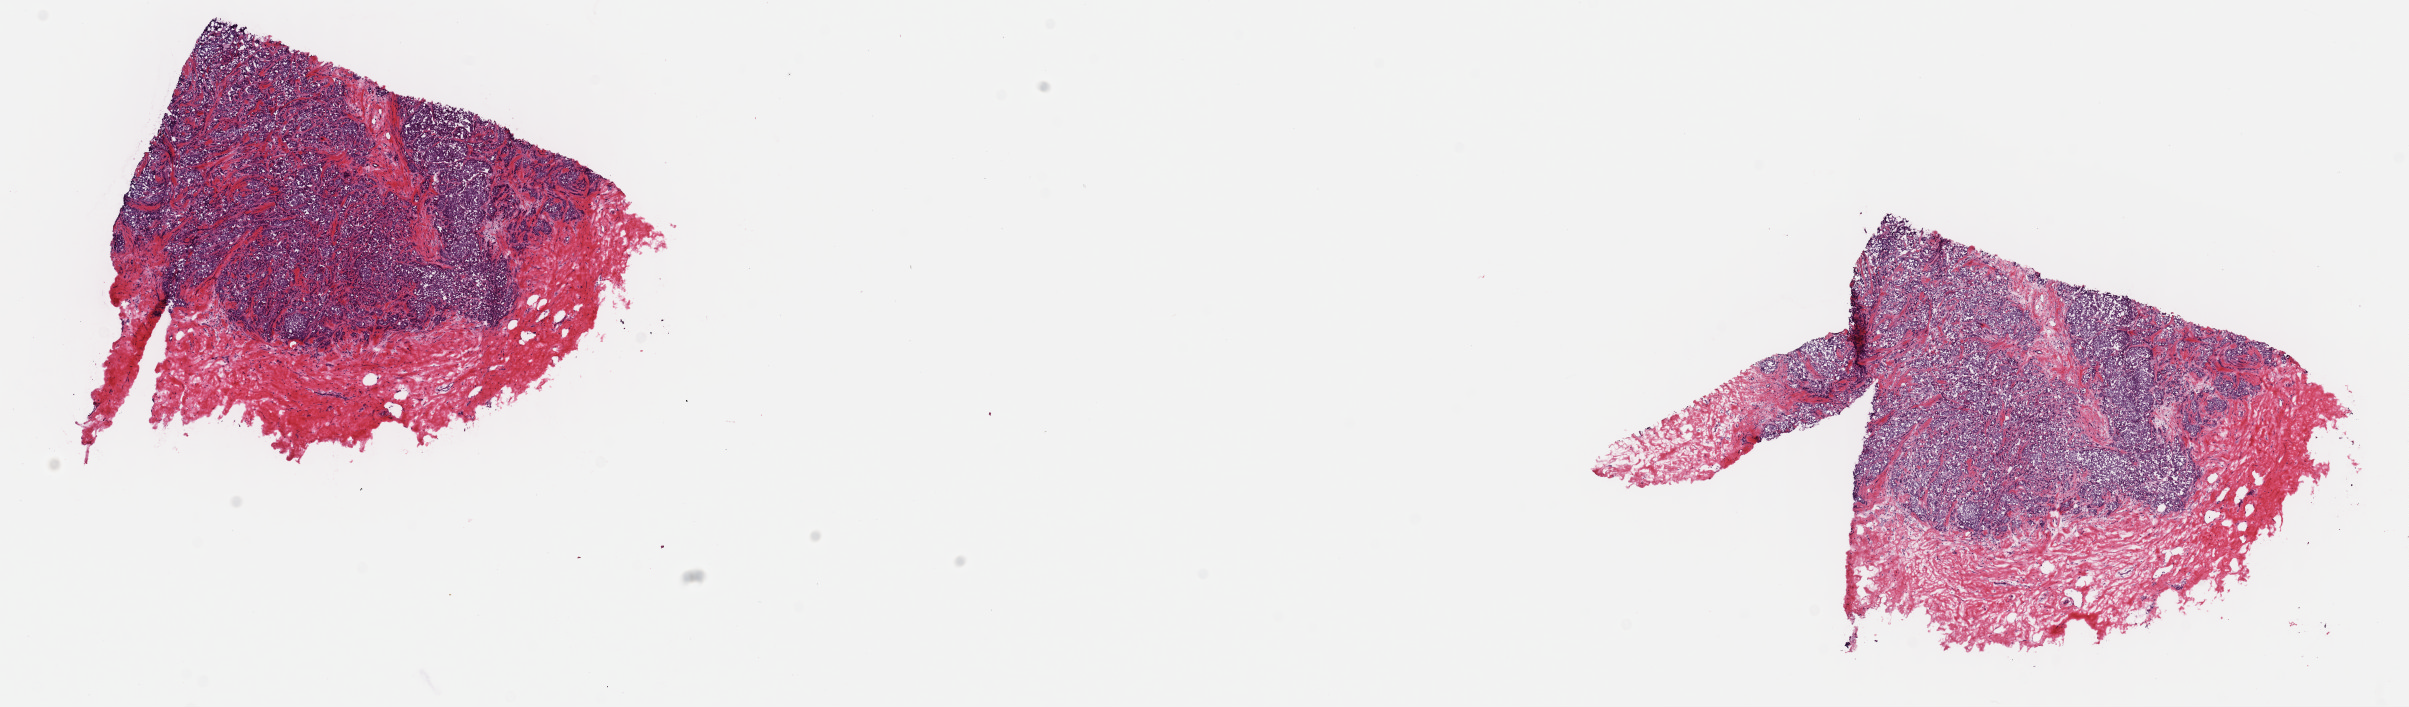
Digitized H&E-stained tissue section (whole slide), shown as a low-resolution overview of the whole scanned area (about 19.0 x 5.6 mm, acquisition: 40x scan); frozen section; sample: primary tumour, breast. Female, age 69 years at initial diagnosis. Composition of this section per pathologist review: tumour cells 65%, tumour nuclei 92%, normal cells 0%, stromal cells 35%, necrosis 0%. Inflammatory infiltration, as recorded: lymphocyte infiltration 1%, monocyte infiltration 0%, neutrophil infiltration 0%.
AJCC pathologic stage: I (5th edition). Diagnosis: Lobular carcinoma, NOS.